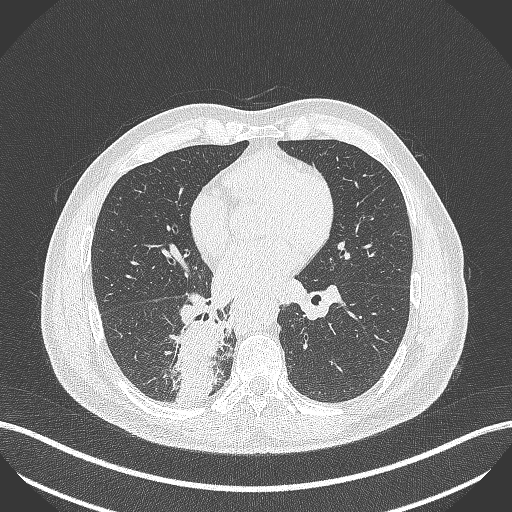
Chest CT, one axial slice. Position 221 of 451 along the scan axis. Reconstruction kernel B70f. 100 kVp. Lung window (W 1500 / L -600 HU). 1 mm slice thickness. 512 × 512 image matrix. Male patient, age 61 years. From the clinical record (not read from this slice): clinical TNM (as recorded): T1 N0 M0.
Structures marked on this image (bounding box drawn by a radiologist):
- lung tumour (recorded histology: small cell carcinoma): bounding box (x1, y1, x2, y2) in pixels: (178, 317, 229, 413)